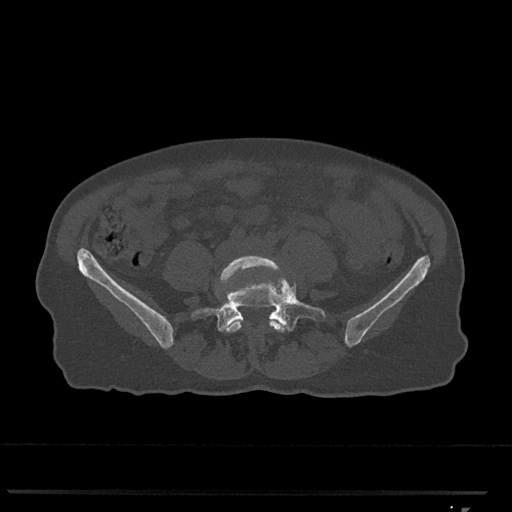
CT including the spine, one axial slice; position 171 of 793 along the scan axis; bone window (W 1800 / L 400 HU); 0.5 mm slice thickness; 512 × 512 image matrix, field of view 380 × 380 mm. Female patient, age 62 years. From the clinical record (not read from this slice): primary cancer: renal.
Structures marked on this image (semi-automatically segmented with operator editing):
- L4 vertebra: bounding box <218,255,286,333> (left, top, right, bottom; pixels)
- L5 vertebra: <191,260,326,332>